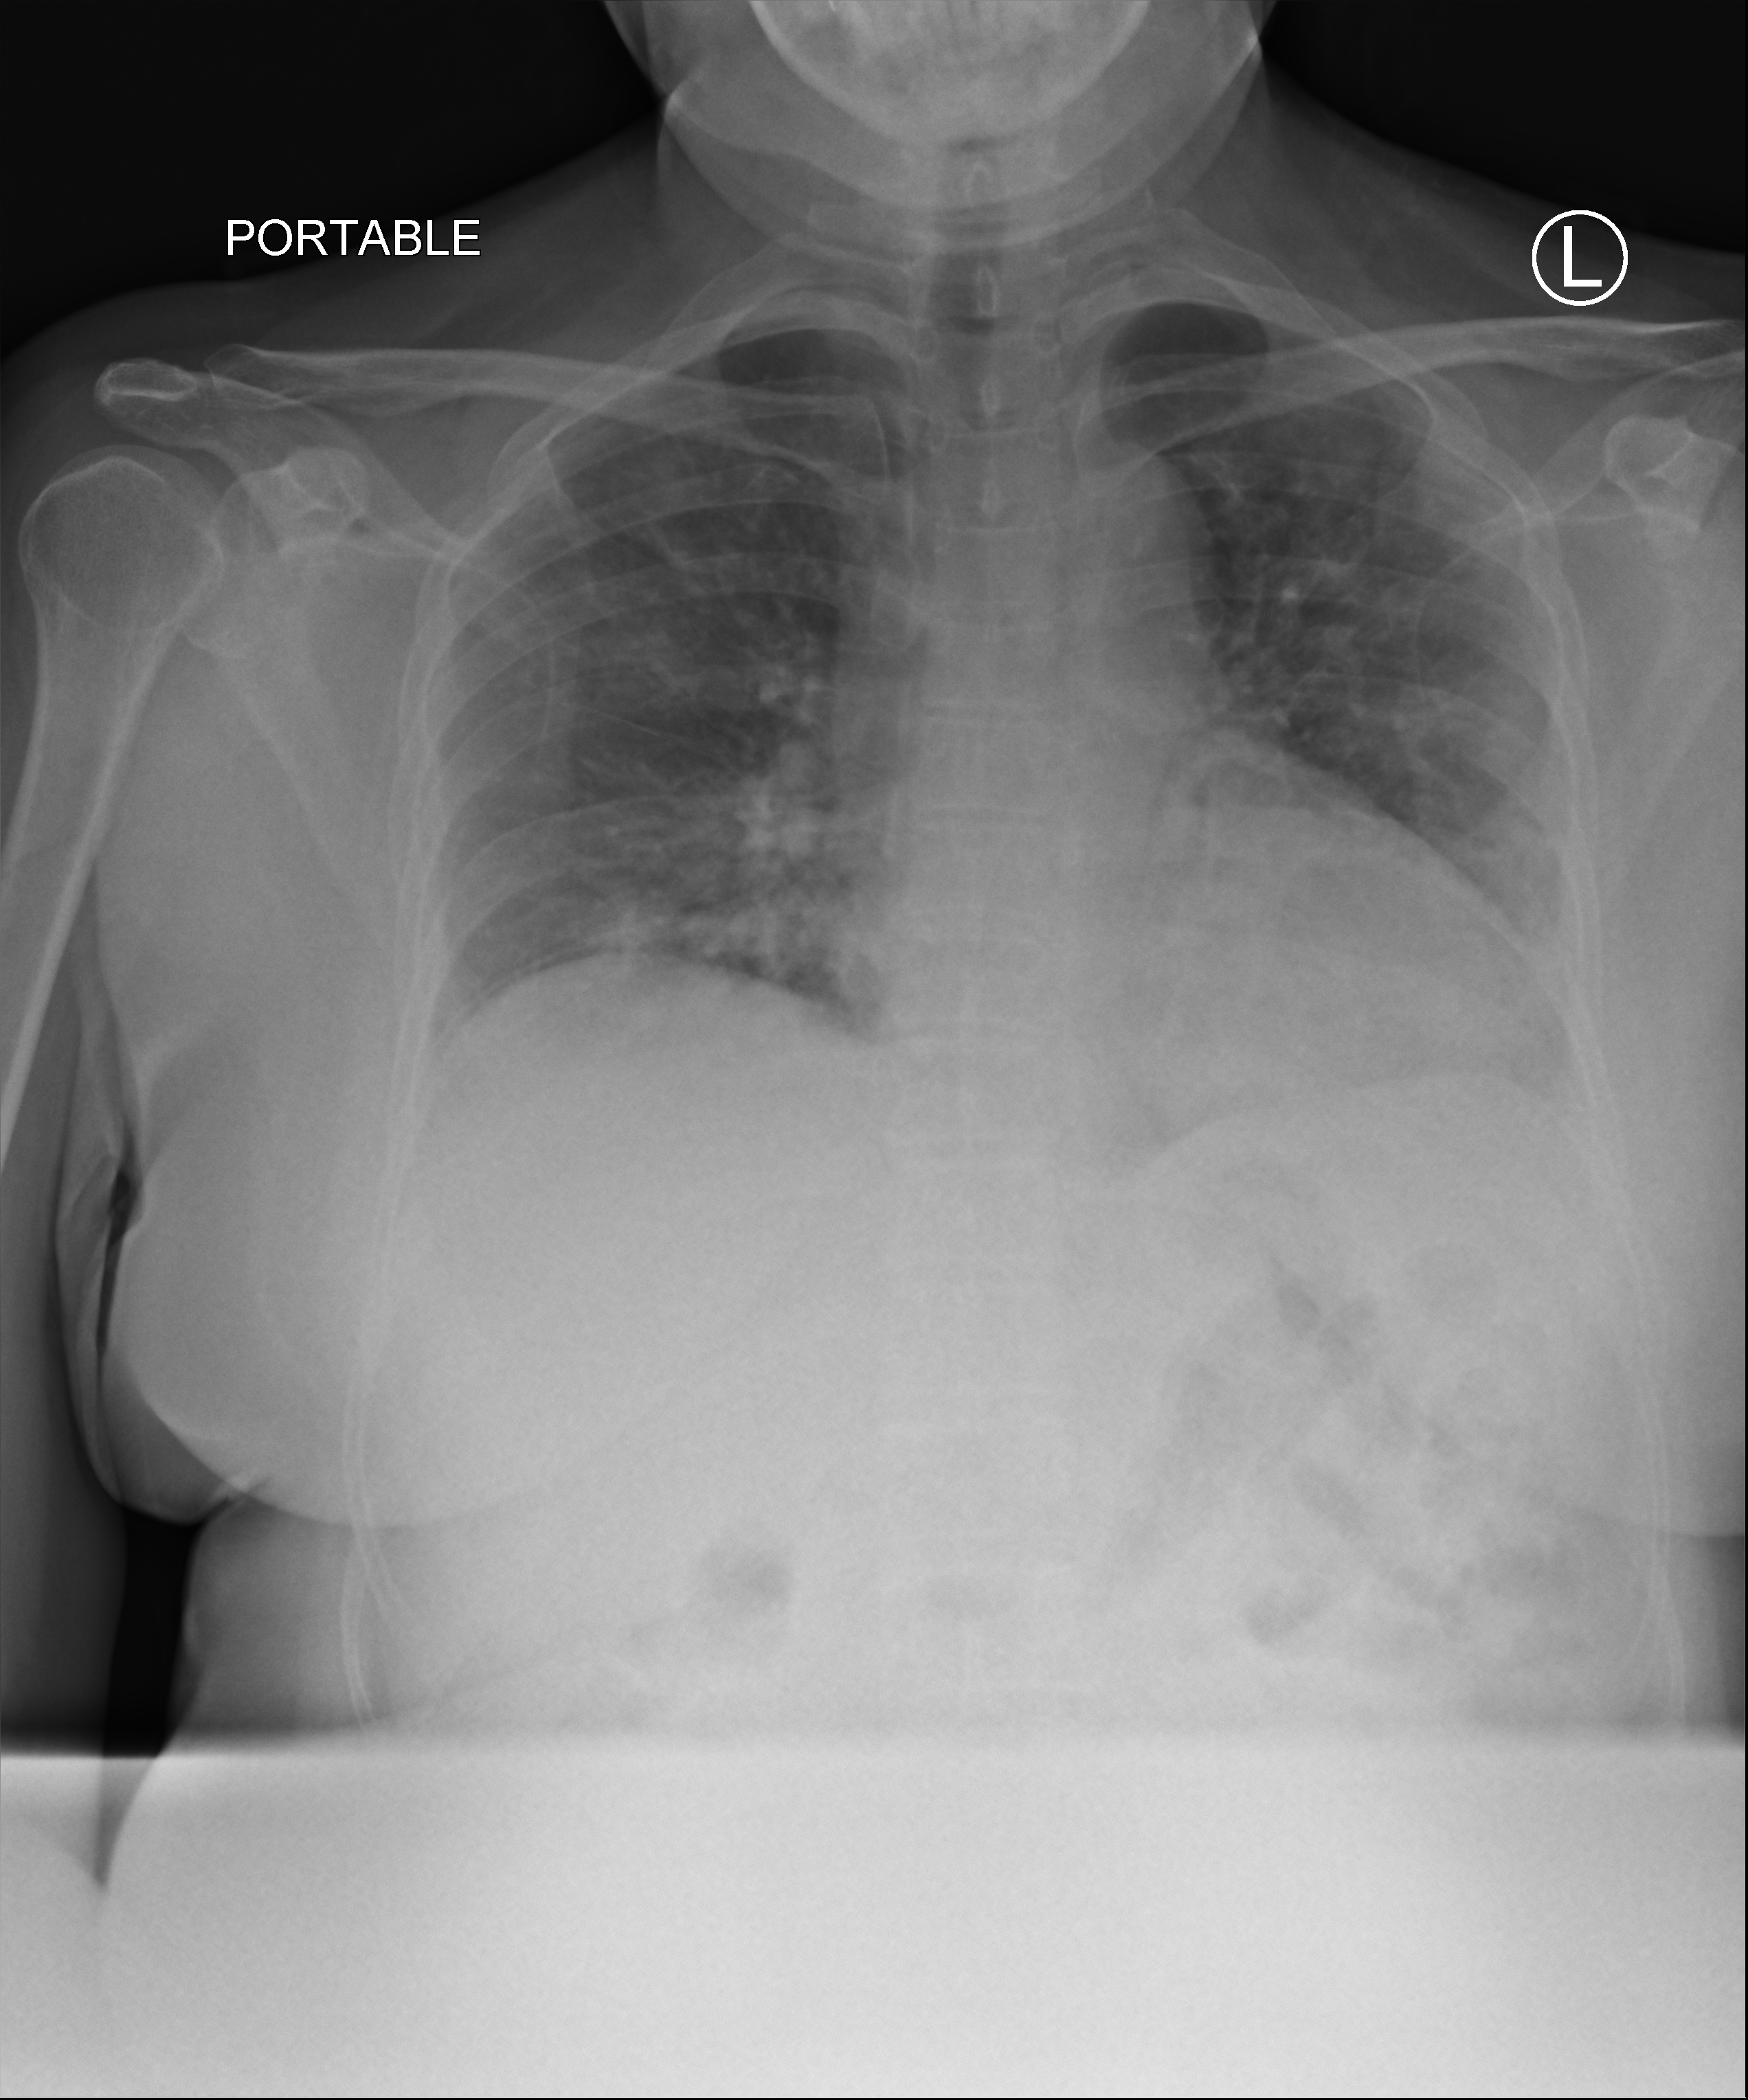
Bedside chest radiograph (computed radiography); anteroposterior (AP) projection. Patient hospitalised with COVID-19; female, aged 18–59 years.
Hospital-stay facts (about this admission, not read from this image; timing relative to this image not recorded): mechanically ventilated during this hospital stay: no; other chronic lung disease (admission record): no.